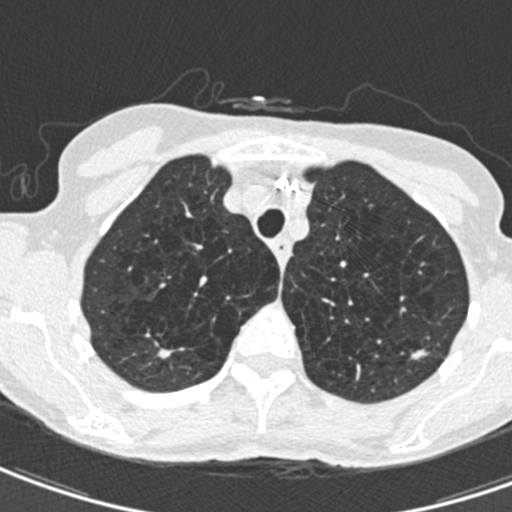
Low-dose screening chest CT, axial slice, second screening round (one year after baseline), lung window (W 1500 / L -600 HU), standard (soft-tissue) reconstruction kernel (B30f), 512 × 512 image matrix, field of view 272 × 272 mm. Female participant, aged 71 years at enrolment.
• Lesion marked by an expert reader, bounding box [x1, y1, x2, y2] px = [405, 332, 444, 370].
• The screening reader recorded 2 non-calcified nodules or masses ≥4 mm on this exam; which of them this box marks is not recorded.